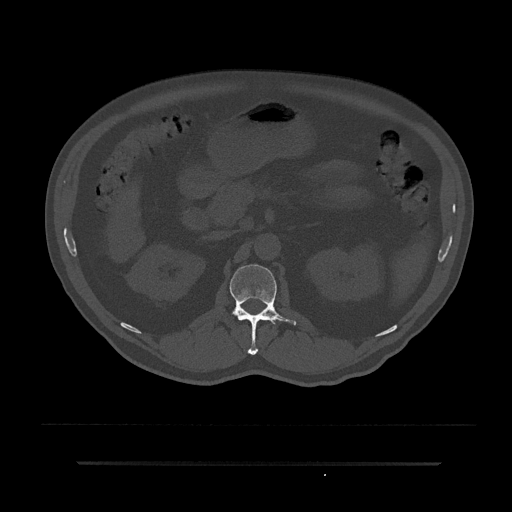
CT including the spine, one axial slice; position 143 of 797 along the scan axis; reconstruction kernel Br40s/3; 120 kVp; bone window (W 1800 / L 400 HU); 0.5 mm slice thickness; 512 × 512 image matrix, field of view 464 × 464 mm. Male patient, age 59 years. From the clinical record (not read from this slice): primary cancer: bile ducts.
Annotated regions visible in this slice (semi-automatic segmentation, software-assisted and operator-edited):
- L1 vertebra: box from (x=230, y=264) to (x=296, y=355) px